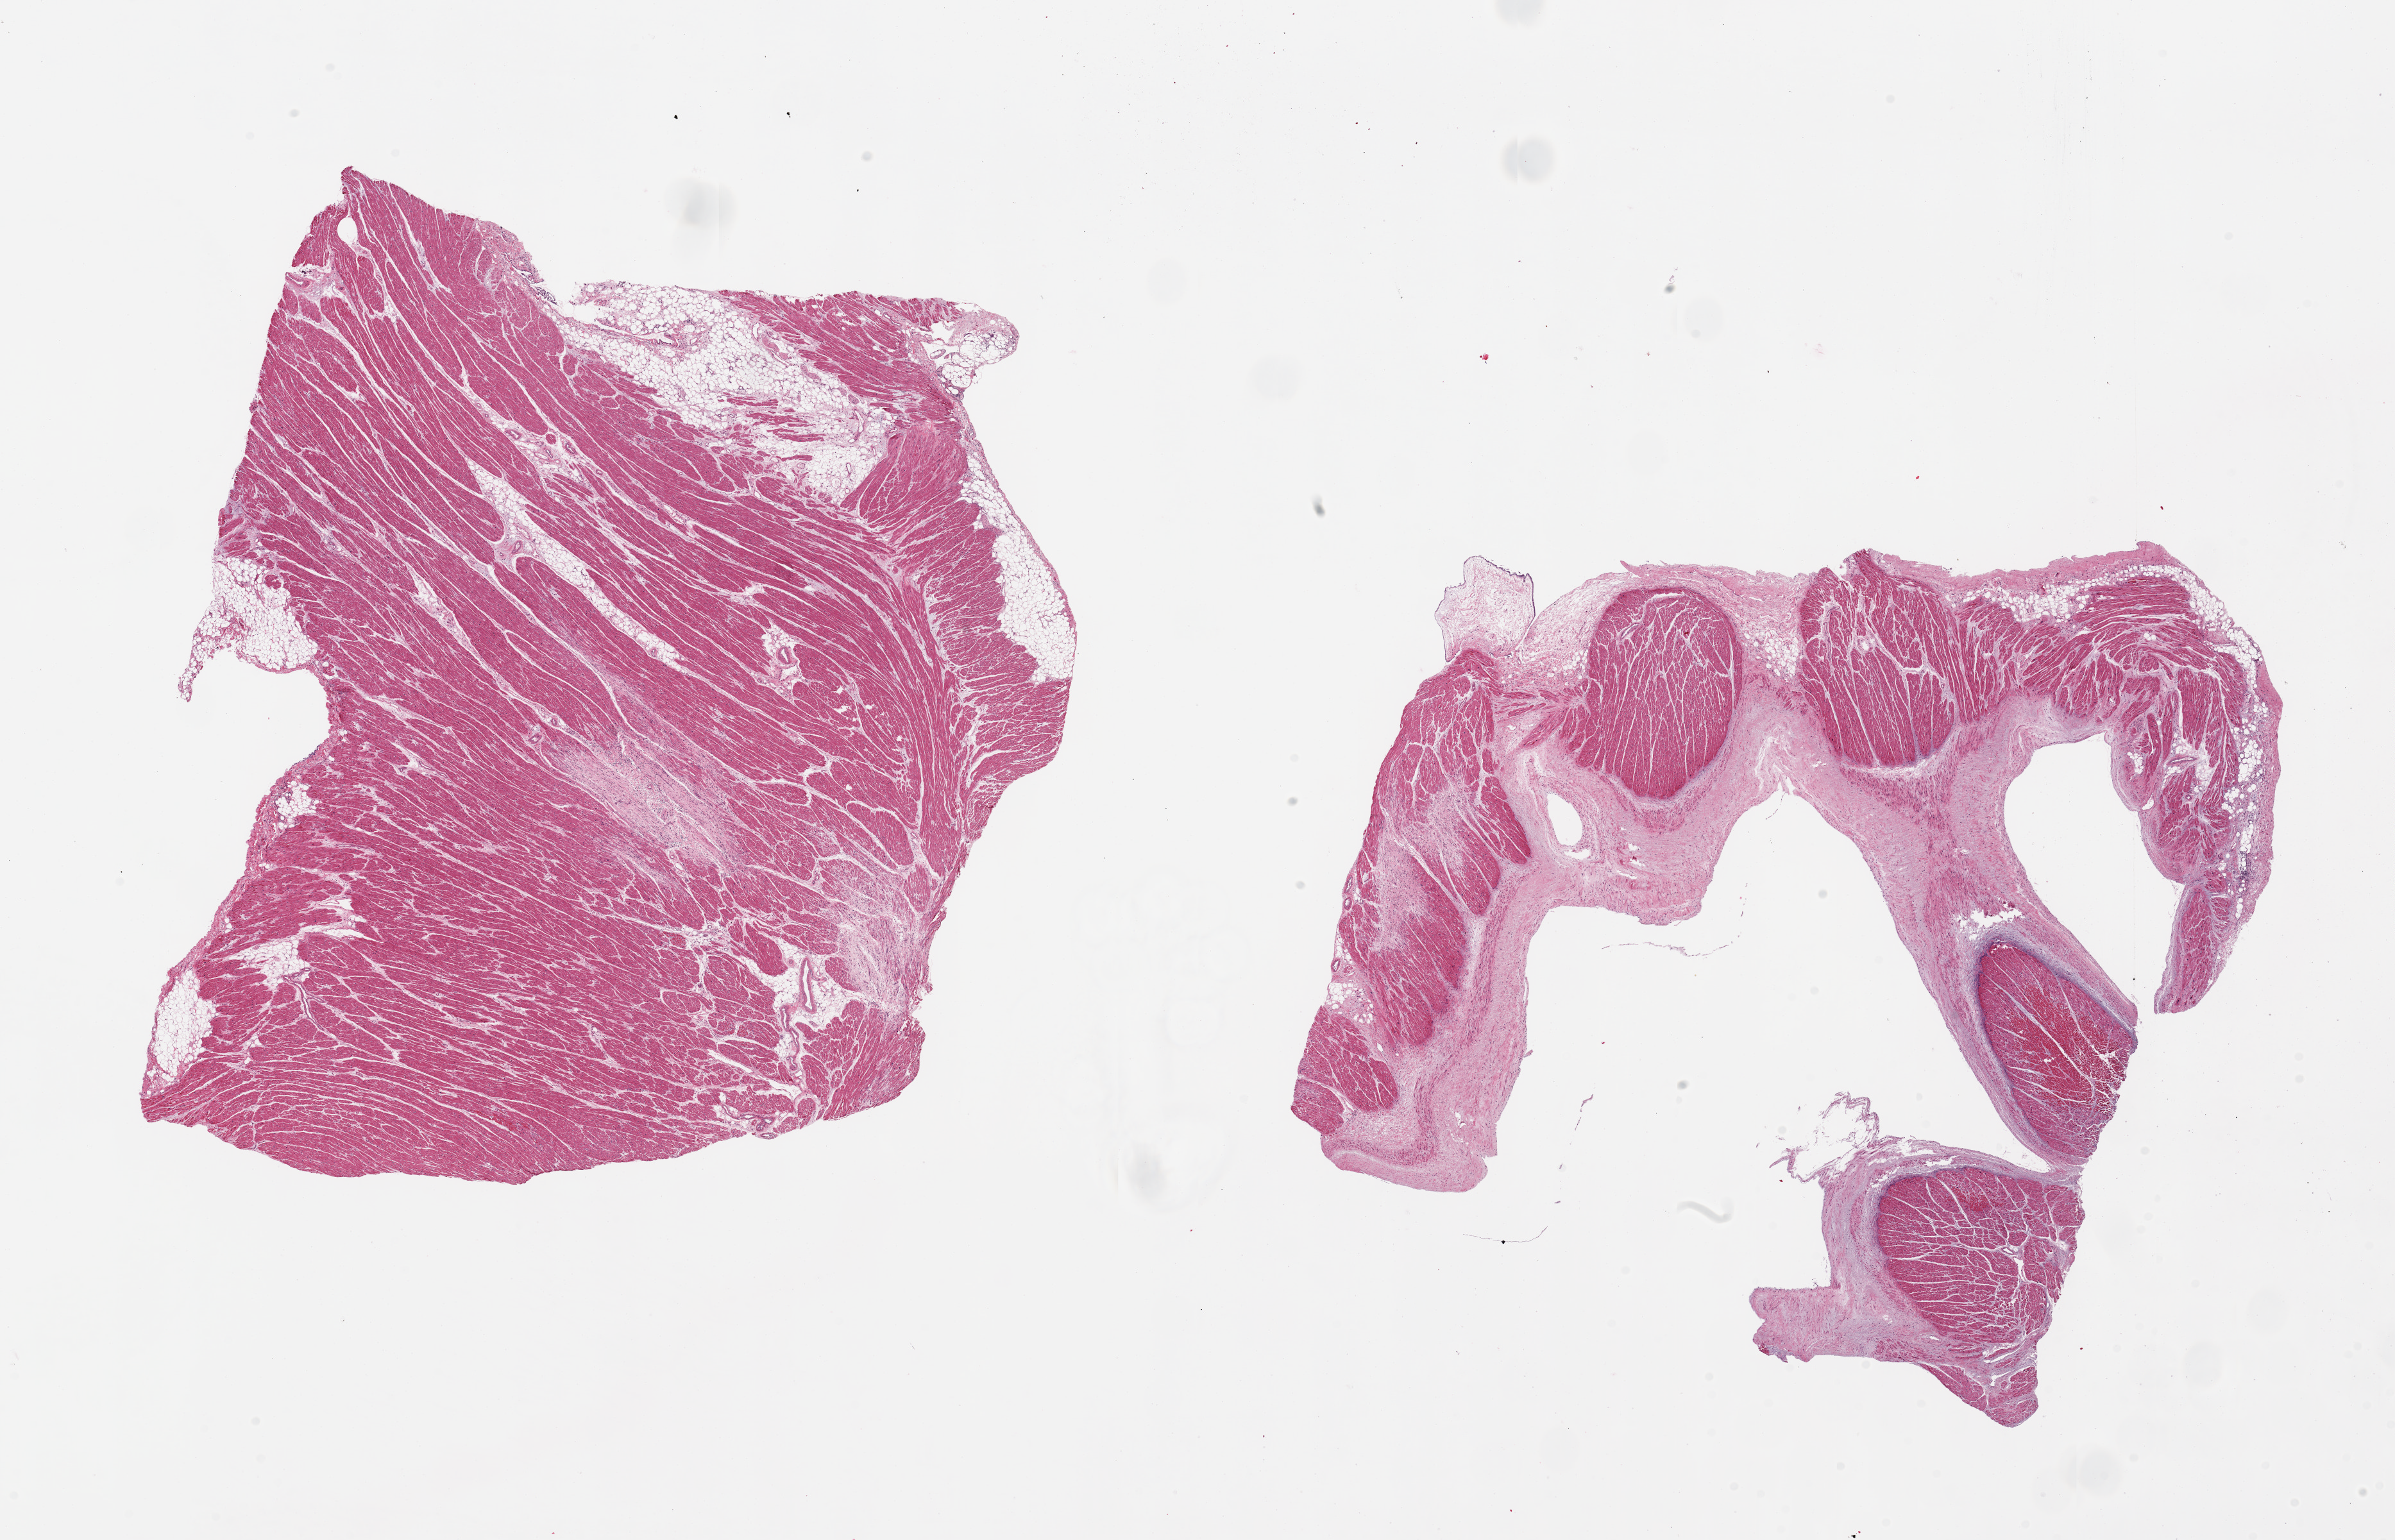
Hematoxylin and eosin (H&E) whole-slide image, a low-resolution overview of the entire scanned area, about 29.5 x 19.0 mm. PAXgene-fixed paraffin-embedded (PFPE) section. Sampled site (target tissue): auricular appendage. Donor tissue sample. Female donor.
- pathologist's review note for this sample: 2 pieces, 12x11 & 11X11mm